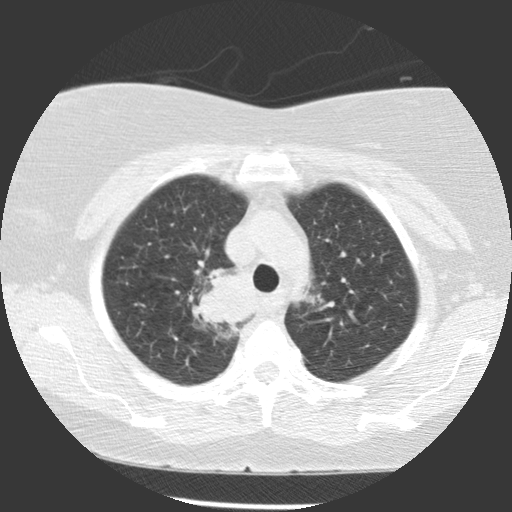
Low-dose screening chest CT, one axial slice. Slice 90 of 116 in the series (ordered by position). 140 kVp. Lung window (W 1500 / L -600 HU). 2.5 mm slice thickness. 512 × 512 image matrix.
Outlined on this slice (outlined manually by an expert reader):
- lesion 1 (tumor, upper lobe of right lung): bounding box [x1, y1, x2, y2] px = [192, 268, 256, 325]